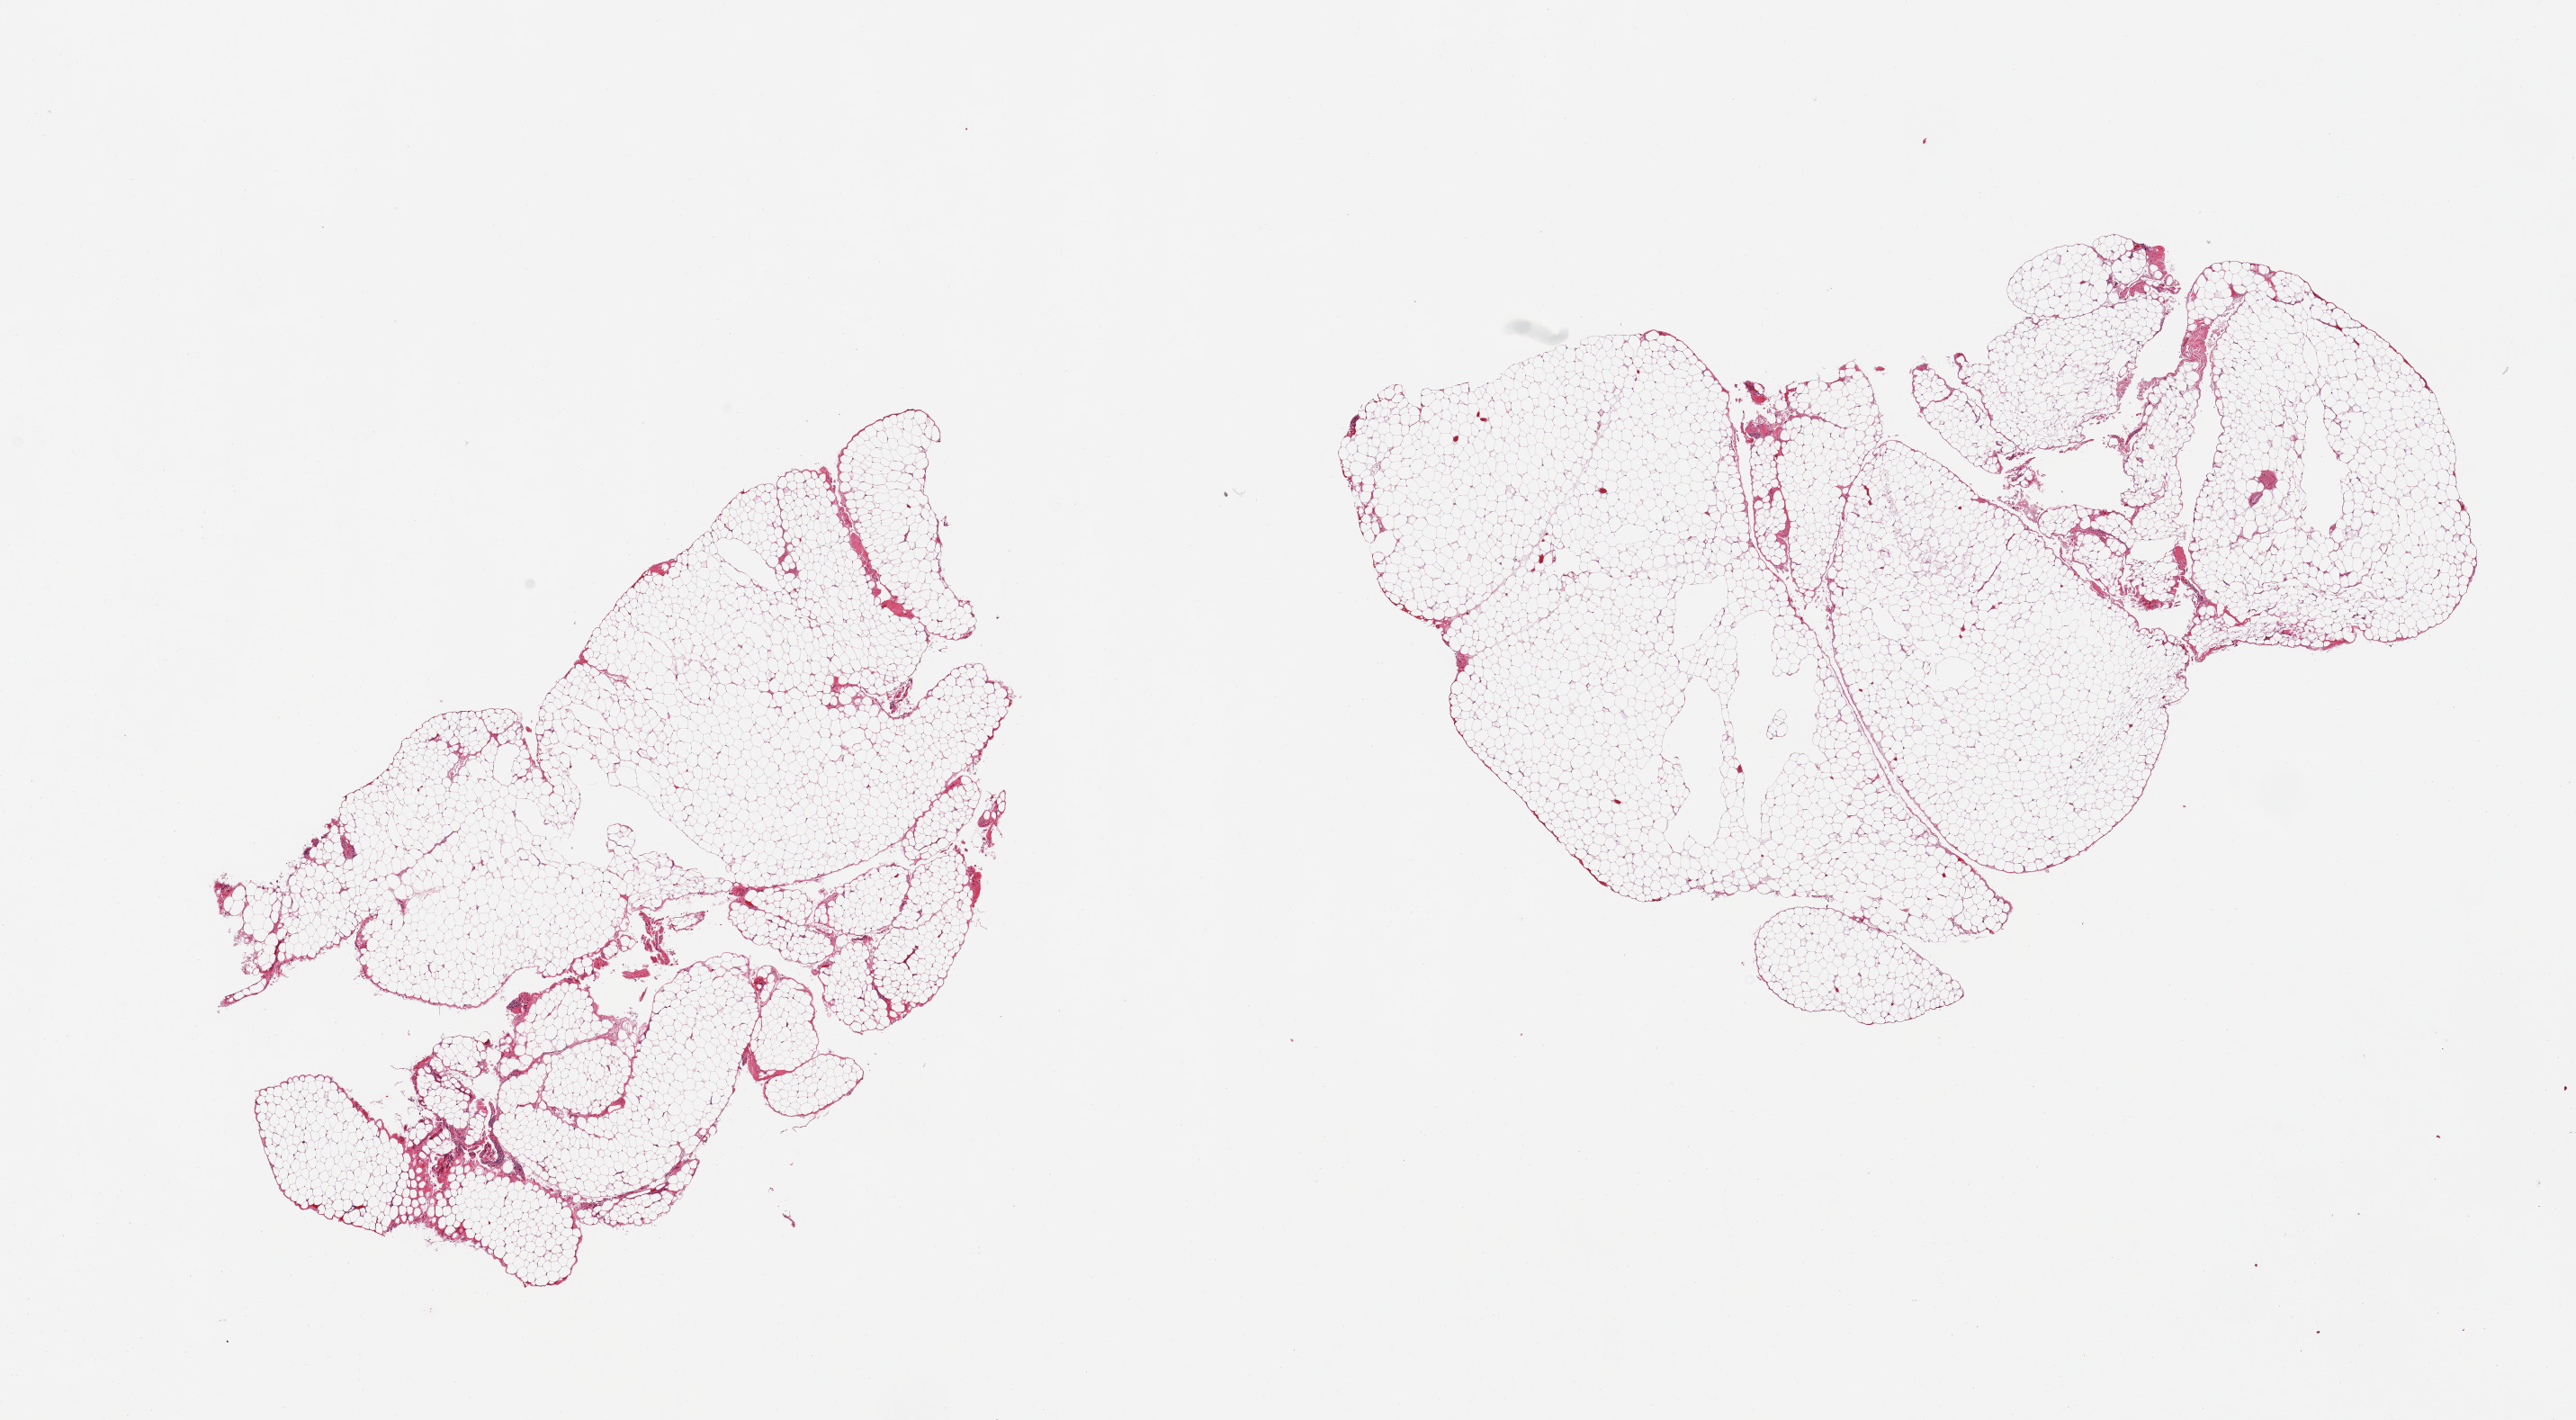
Digitized haematoxylin and eosin-stained section, brightfield, shown as a low-resolution overview of the whole scanned area (about 22.6 x 12.5 mm, acquisition: 20x scan), PAXgene-fixed, paraffin-embedded tissue, section of omentum (target tissue), donor tissue sample. Donor sex: male.
- review note (as recorded): 2 pieces; minimal stromal content